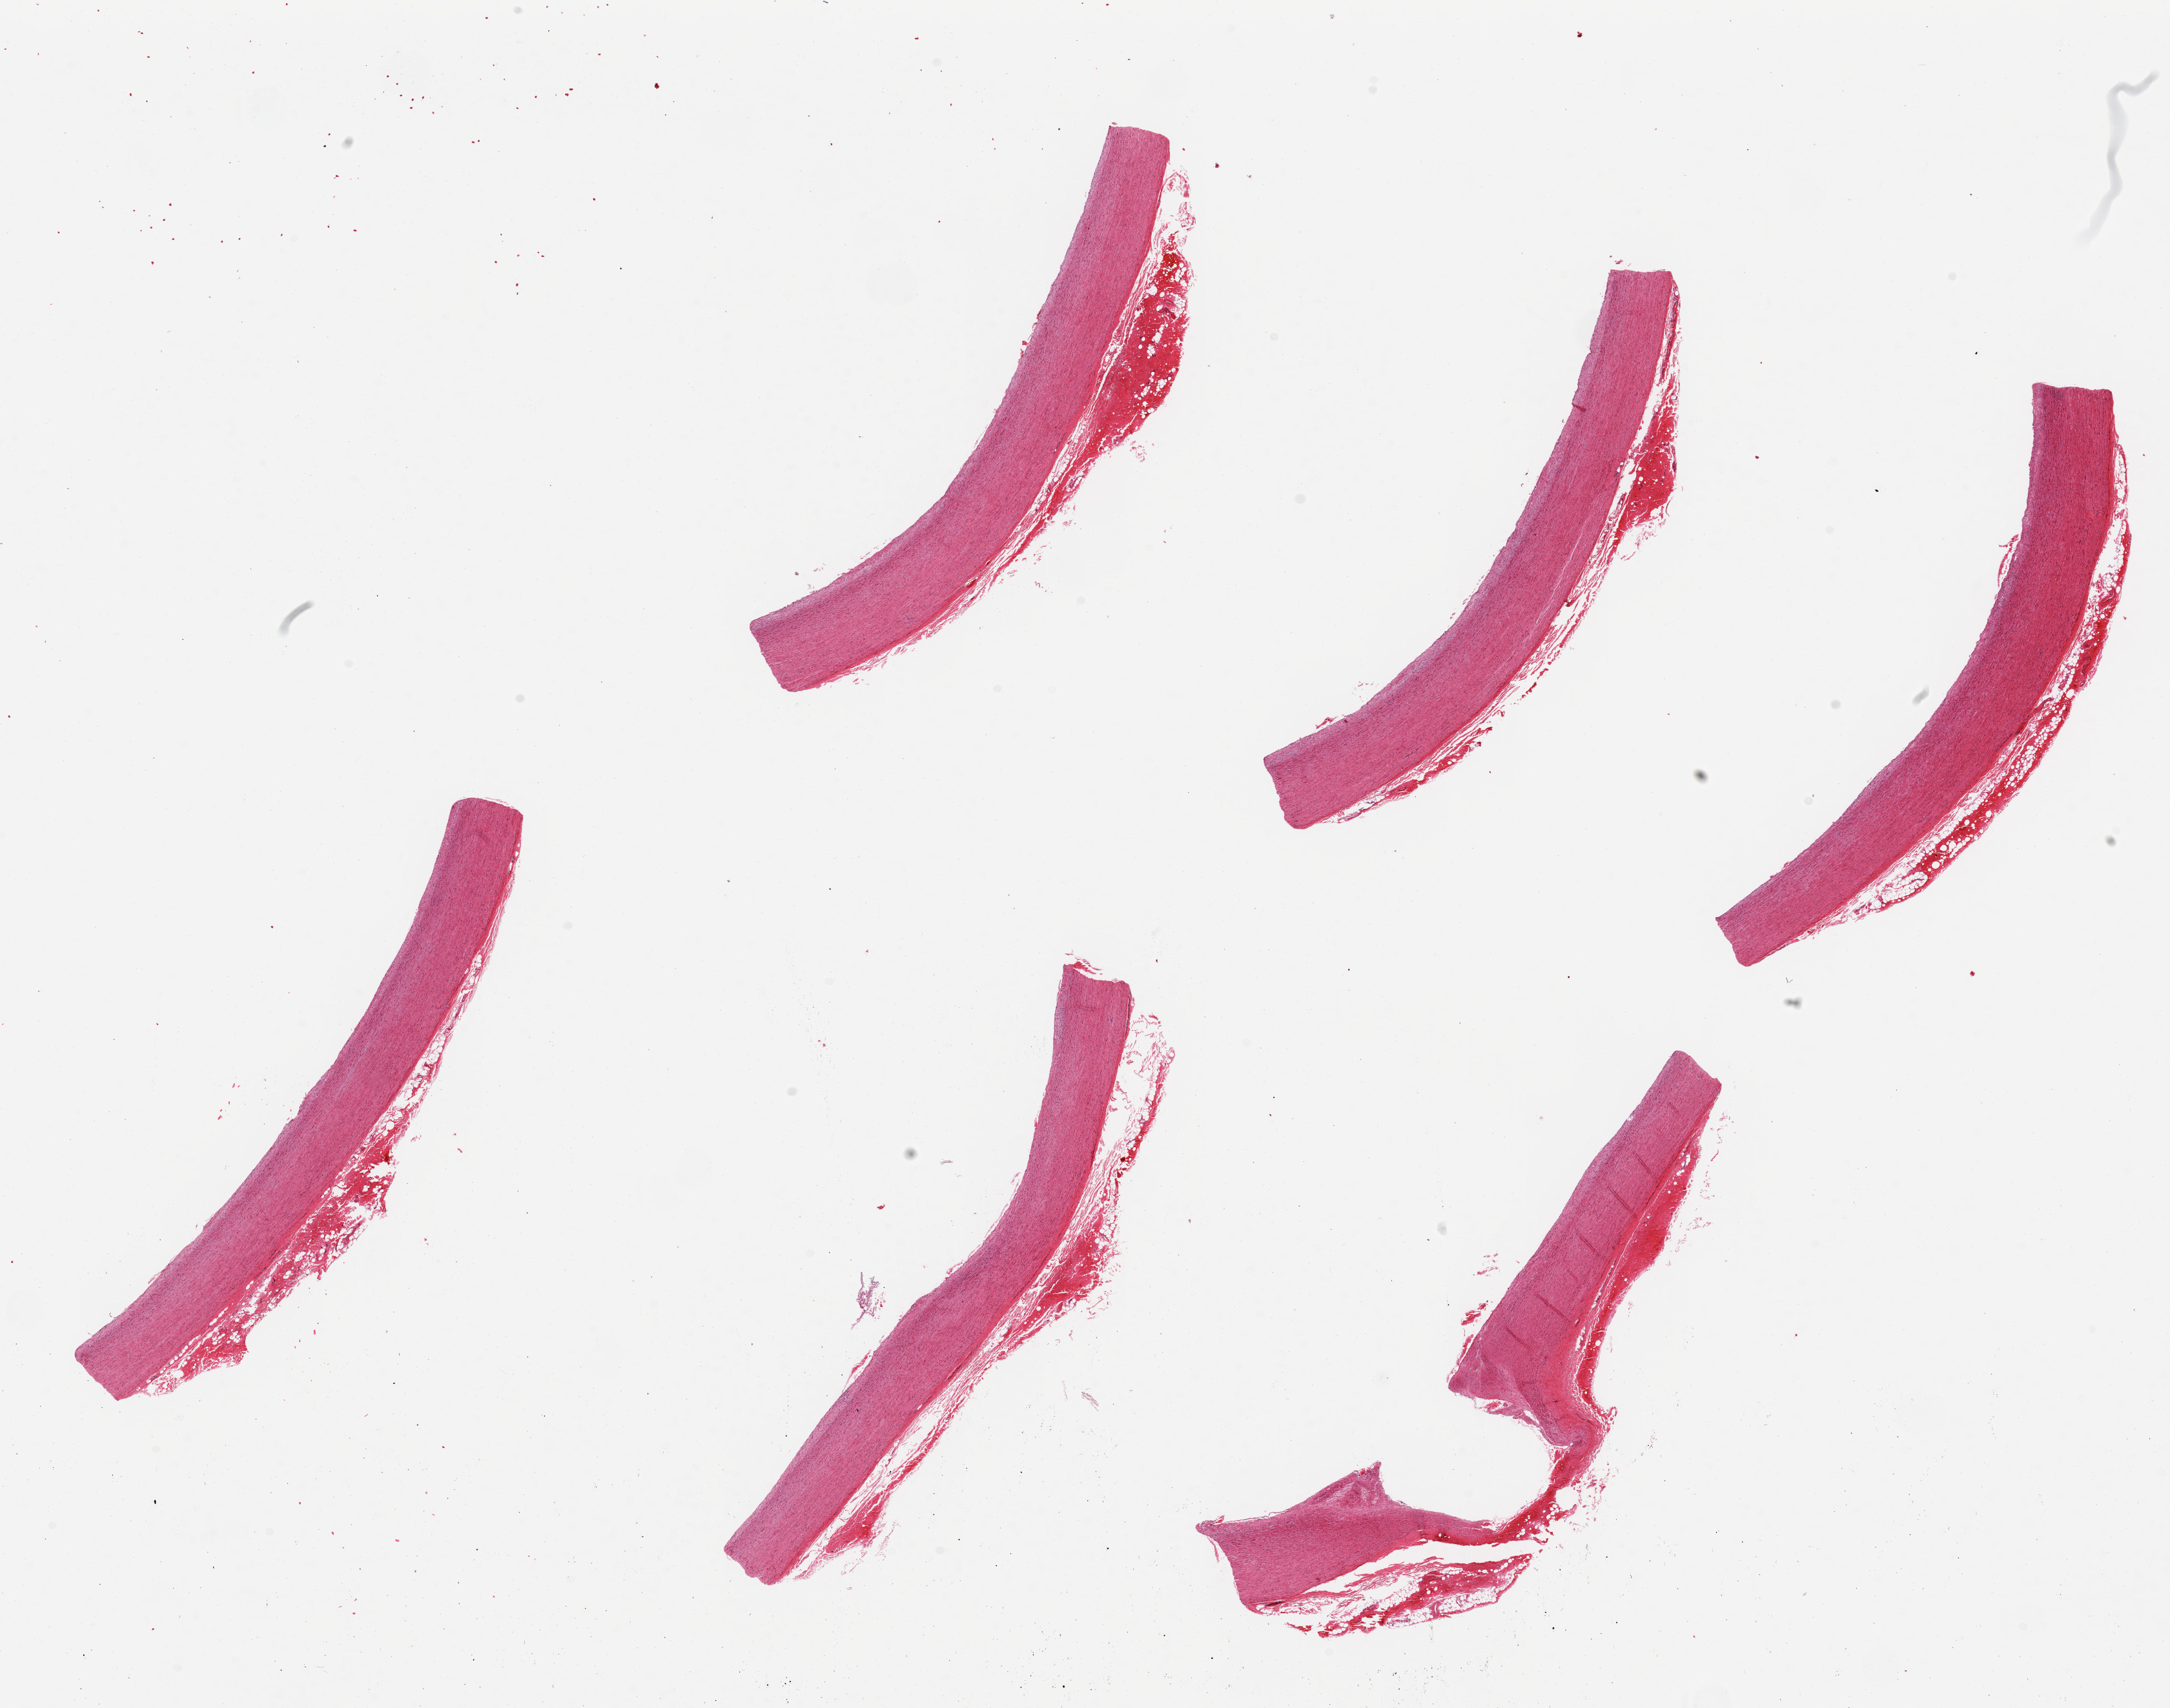
Whole-slide image, haematoxylin and eosin stain — shown as a low-resolution overview of the whole scanned area (about 26.6 x 20.9 mm, slide scanned at 20x). PAXgene-fixed paraffin-embedded (PFPE) section. Sampled site (target tissue): aorta. Donor tissue sample. Donor: male.
• pathologist's review note for this sample: 6 pieces up to 8.5x1 mm; recent adventitial hemorrhage in all, up to 20% of piece